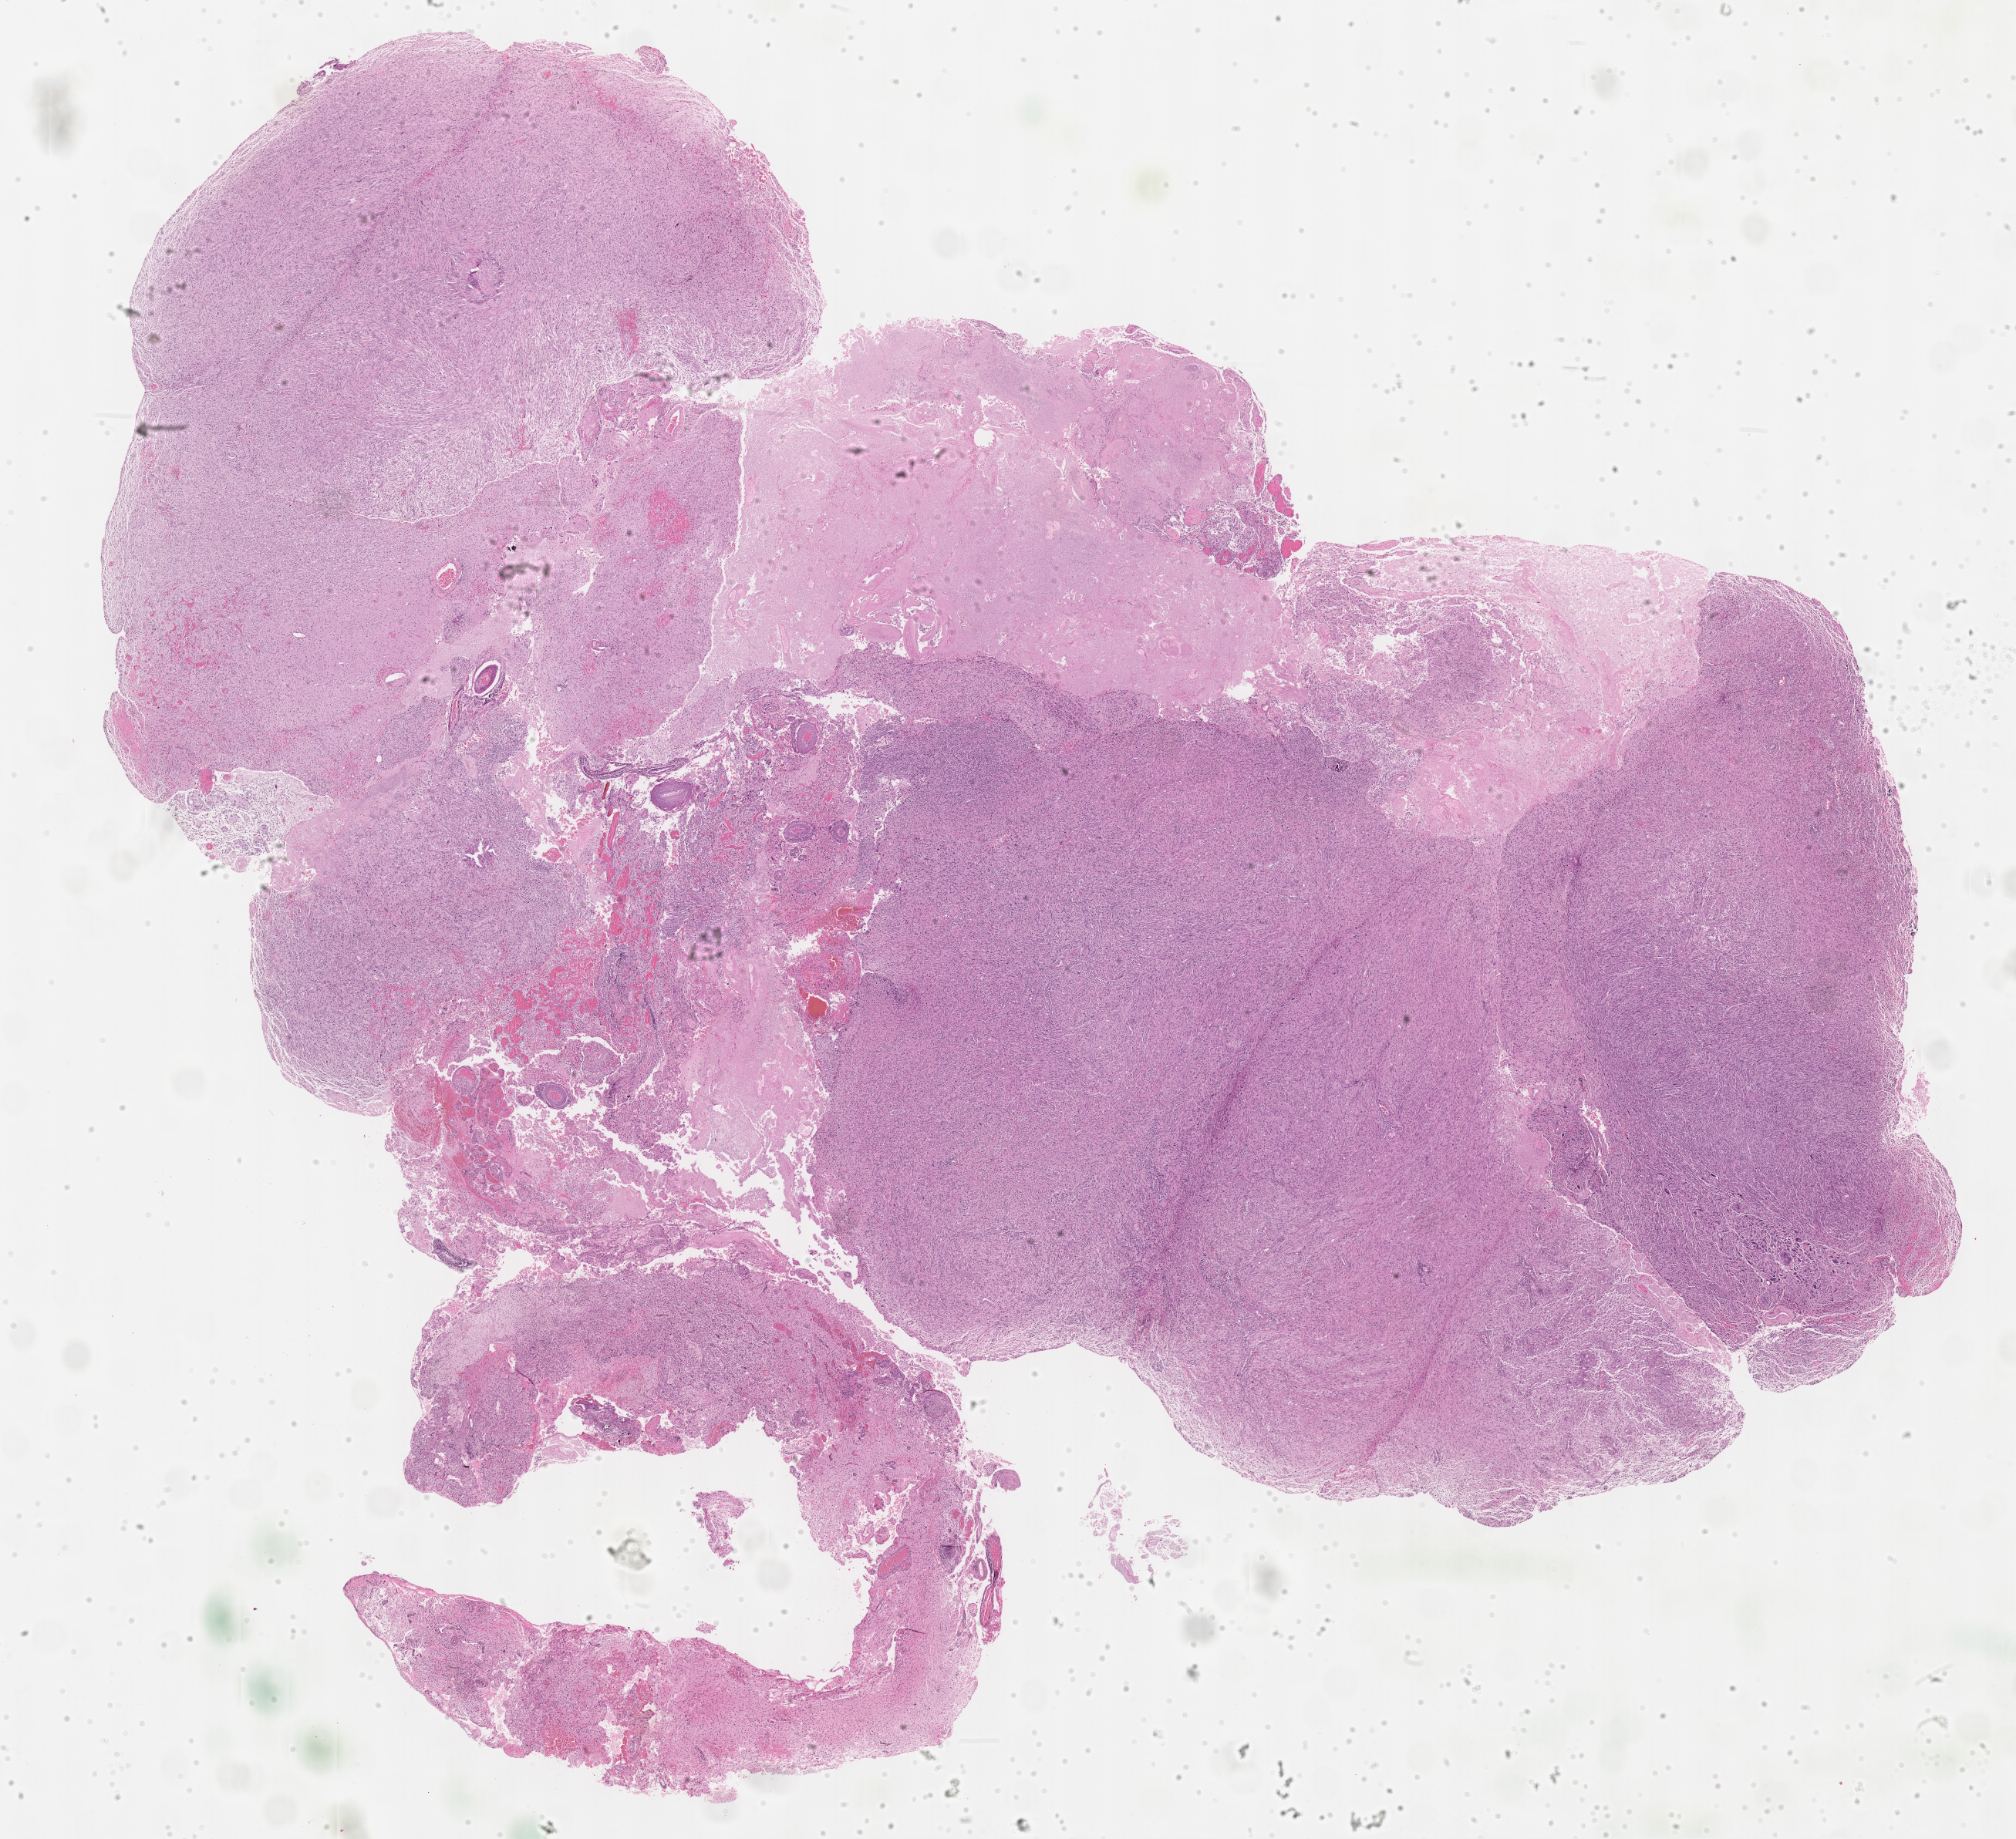
Whole-slide histology image, H&E-stained, whole scanned area (about 21.2 x 19.3 mm) shown as a low-resolution overview, formalin-fixed paraffin-embedded (FFPE) diagnostic section, brain, primary tumour sample. Female patient; age at initial diagnosis 33 years.
• histologic diagnosis: Glioblastoma